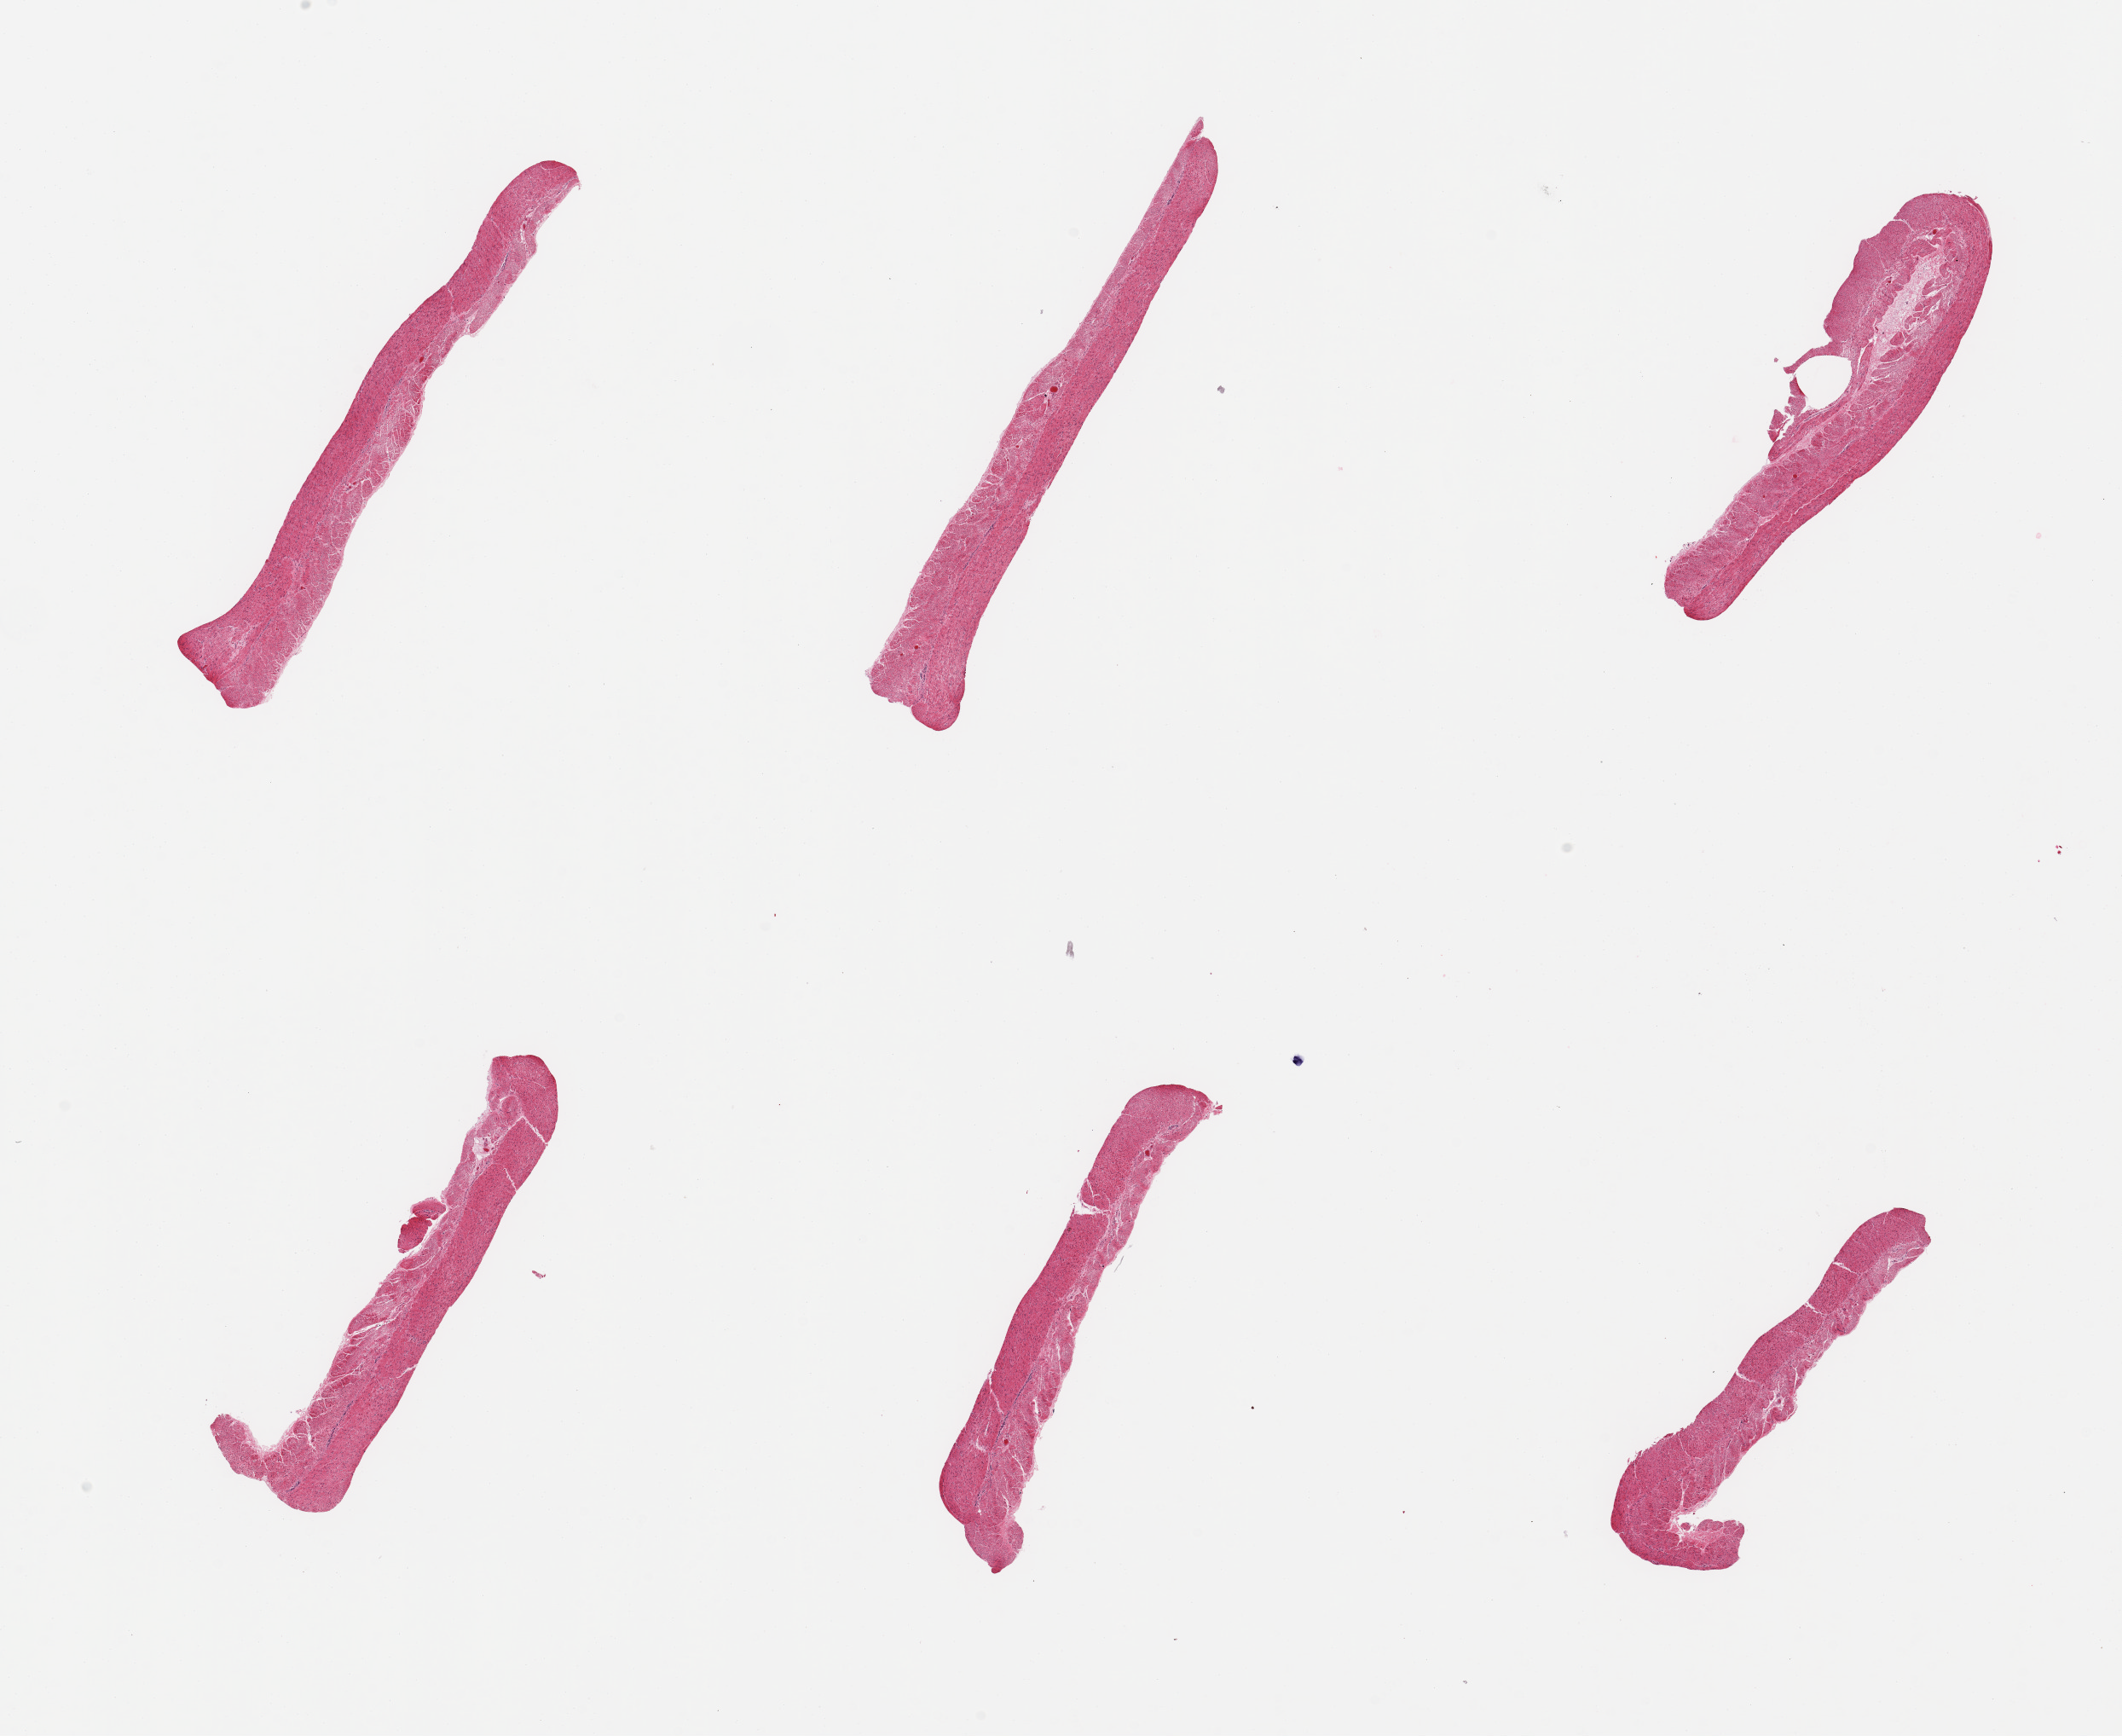
Whole-slide image, hematoxylin and eosin (H&E) stain — a low-resolution overview of the entire scanned area, about 19.7 x 16.1 mm; PAXgene-fixed, paraffin-embedded tissue; sampled site (target tissue): sigmoid colon; tissue donor sample. Donor sex: female.
• pathologist's review note for this sample: 6 pieces; target muscularis